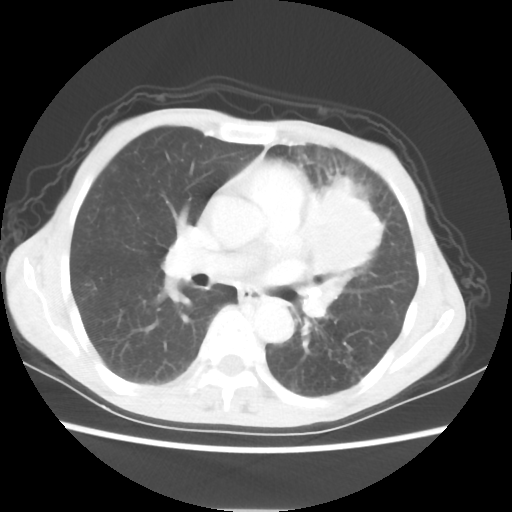
Chest CT, one axial slice; slice 33 of 56 in the series (ordered by position); reconstruction kernel STANDARD; 80 kVp; lung window (W 1500 / L -600 HU); 5 mm slice thickness; 512 × 512 image matrix, field of view 331 × 331 mm. Female patient, age 60 years. From the clinical record (not read from this slice): clinical TNM (as recorded): T4 N1 M0.
Structures marked on this image (bounding box drawn by a radiologist):
- lung tumour (recorded histology: adenocarcinoma): bounding box (x1, y1, x2, y2) in pixels: (305, 169, 401, 286)